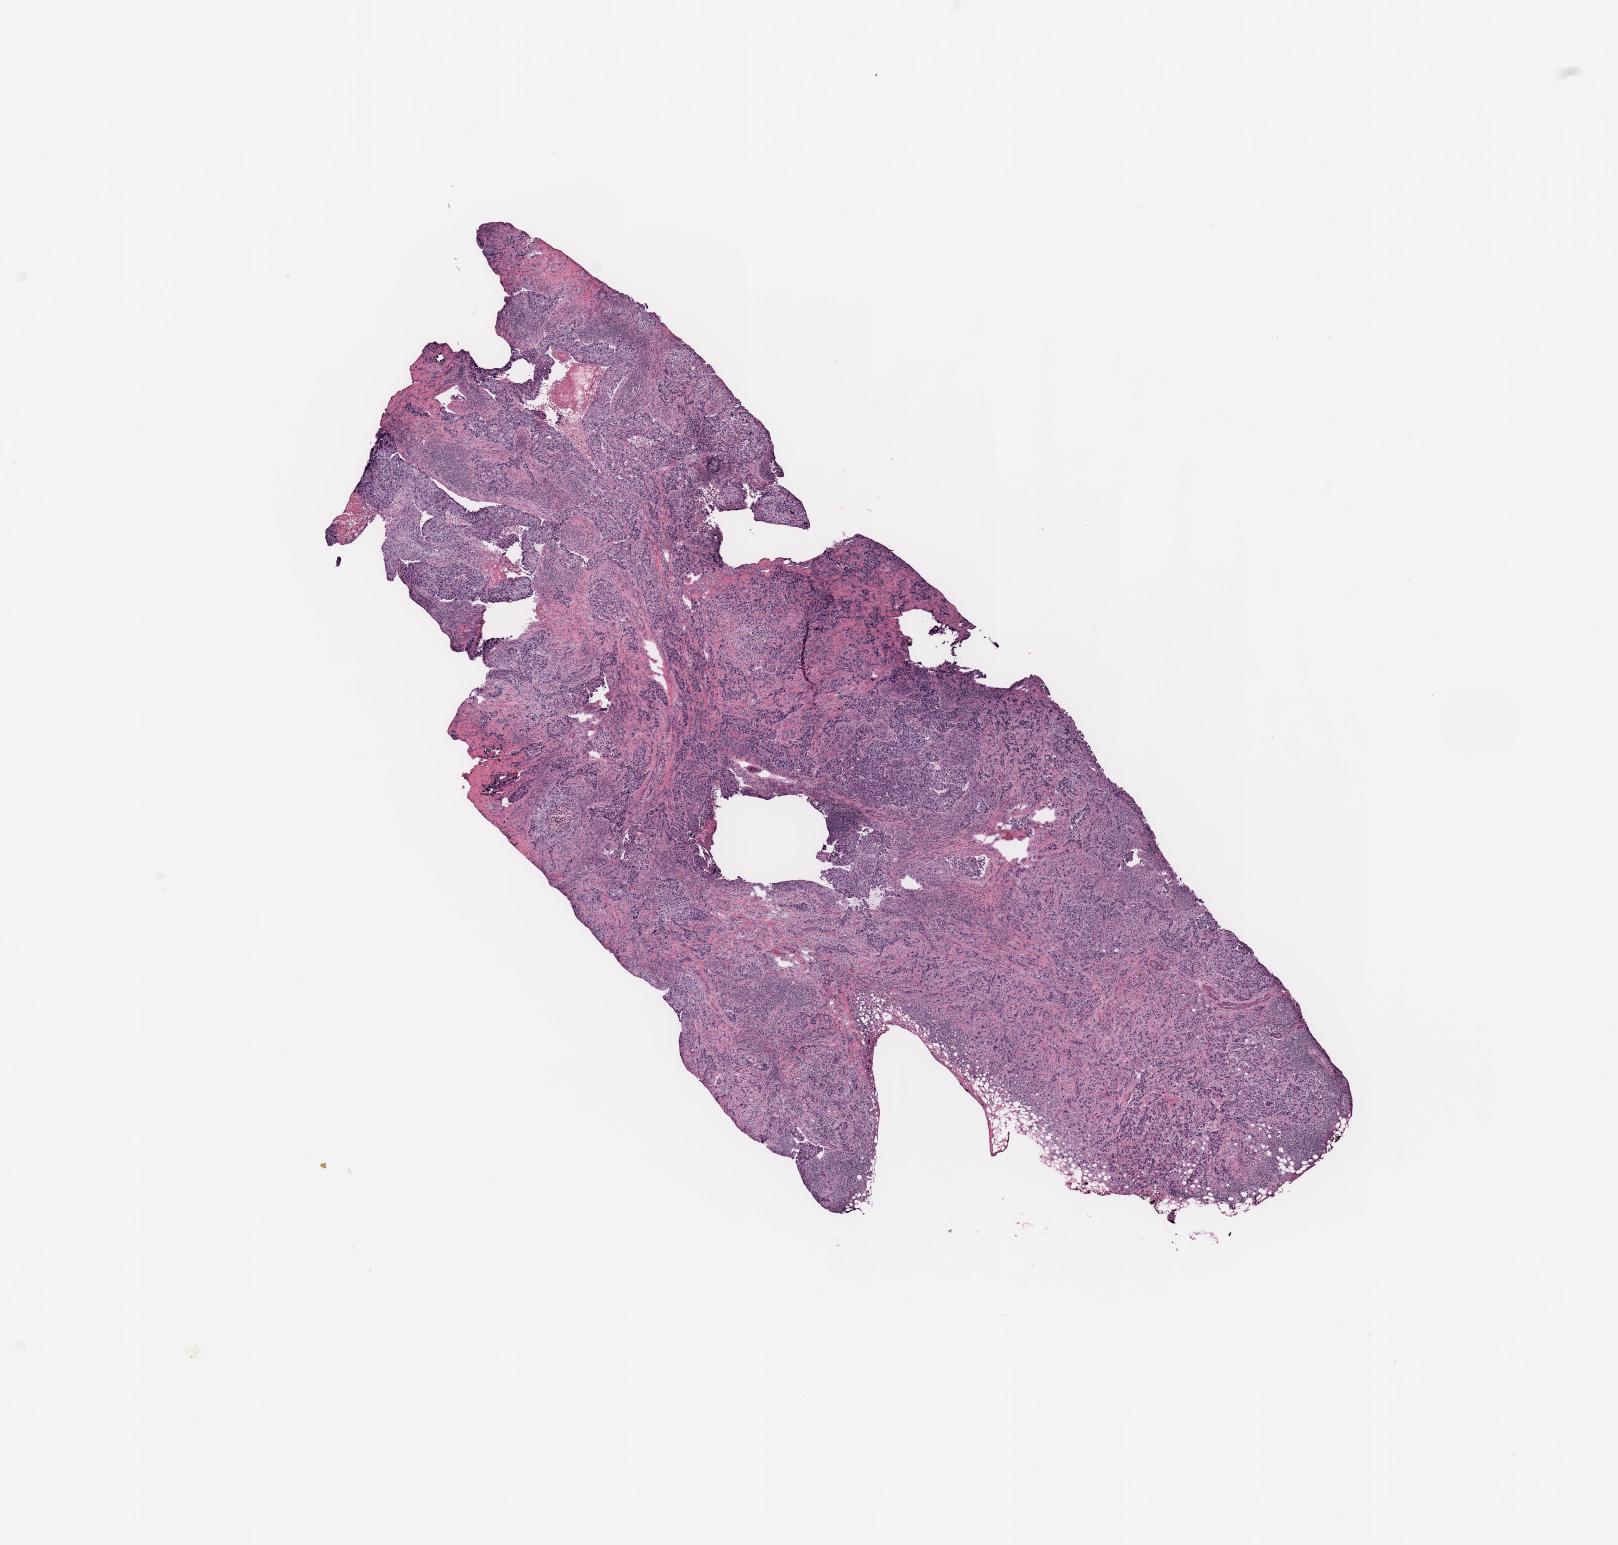
H&E-stained whole-slide image, low-resolution overview of the scanned area, about 12.8 x 12.2 mm (acquisition: 20x scan); breast, tissue type not recorded.
Patient diagnosis (cohort enrolment): breast cancer (breast).